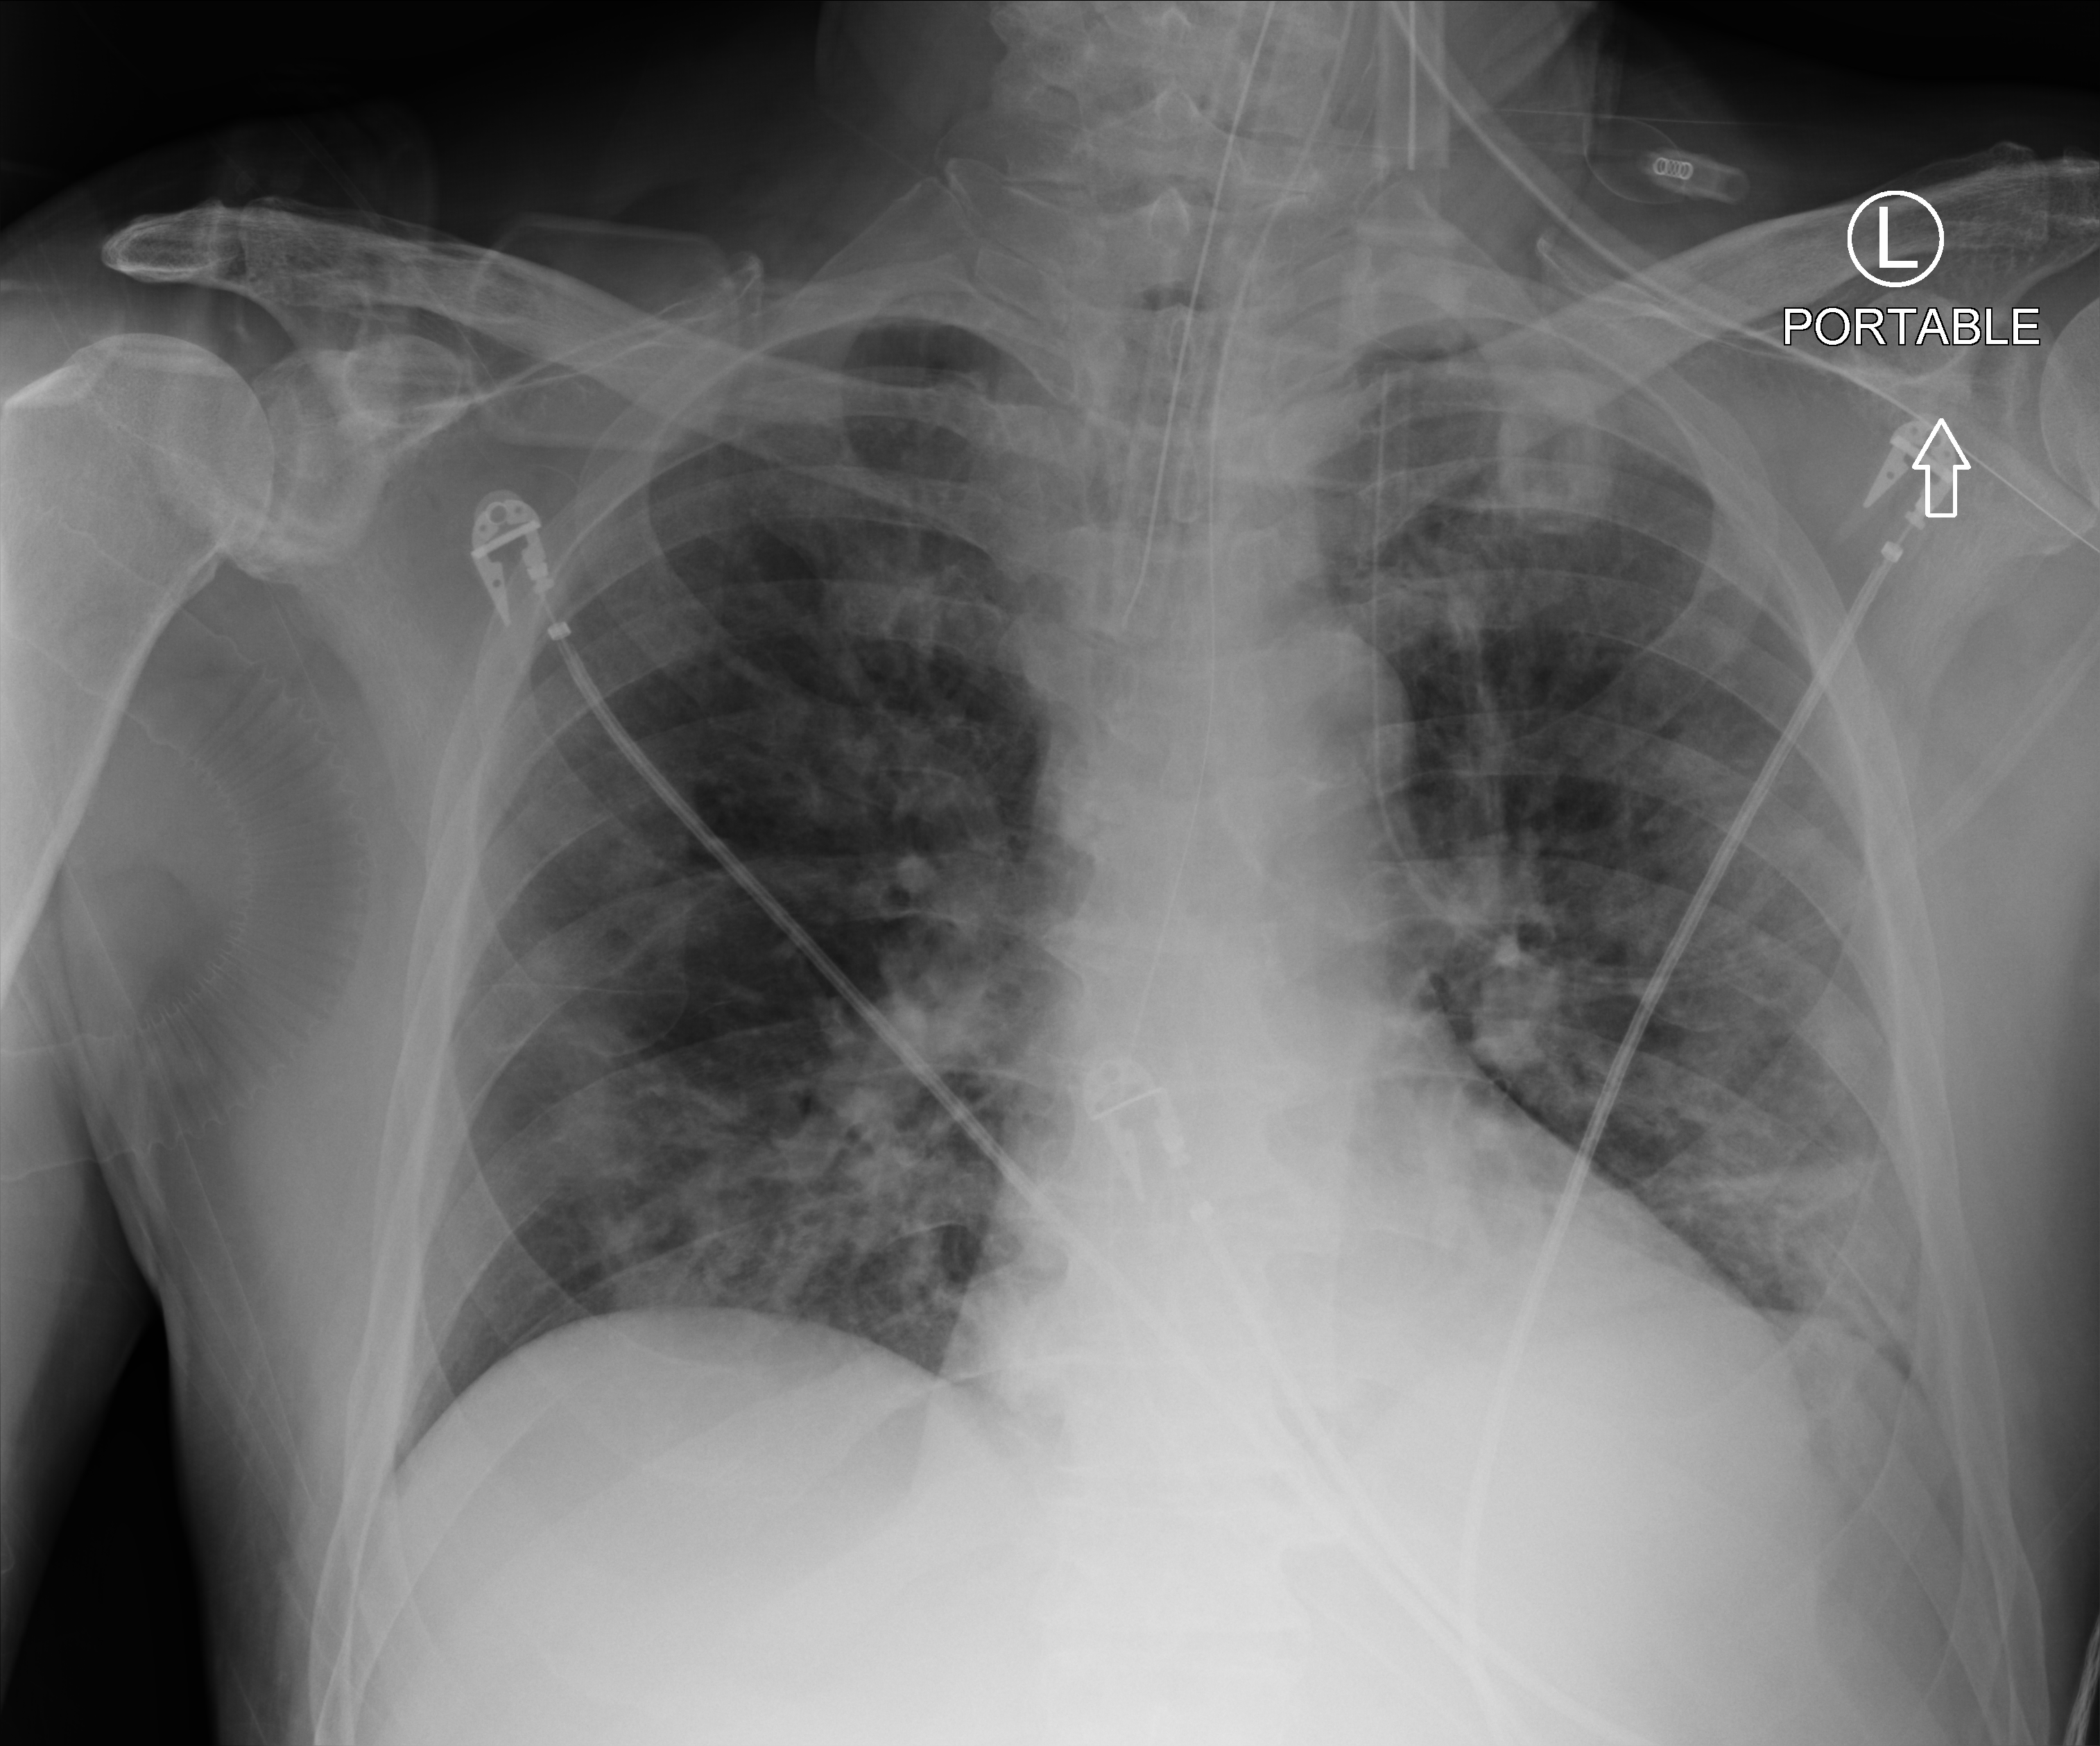
Bedside chest radiograph (computed radiography), anteroposterior (AP) projection. Patient hospitalised with COVID-19; male, aged 60–74 years.
Admission-level facts for this patient (not findings on this image; timing relative to this image not recorded):
- admitted to intensive care during this hospital stay: yes
- mechanically ventilated during this hospital stay: yes
- diabetes (admission record): yes